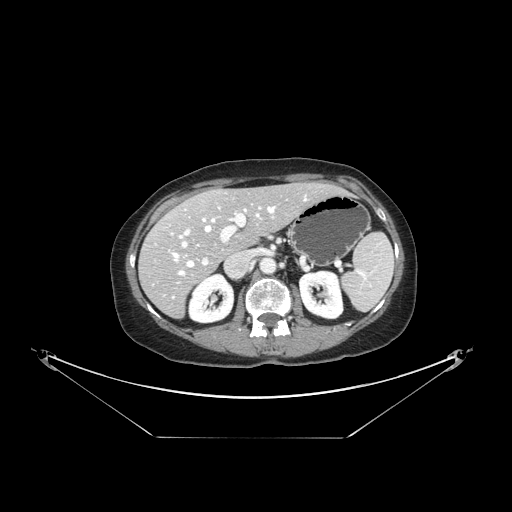
Contrast-enhanced abdominal CT, one axial slice; position 87 of 148 along the scan axis; intravenous contrast given; soft-tissue window (W 400 / L 40 HU); 2.5 mm slice thickness; 512 × 512 image matrix. Female patient, age 73 years. From the clinical record (not read from this slice): diagnosis: colorectal cancer liver metastases, imaged before liver resection; multiple liver metastases: no; largest metastasis: 1 cm; disease in both lobes: no.
Structures marked on this image (expert manual segmentation):
- hepatic veins: bounding box <173,198,306,275> (left, top, right, bottom; pixels)
- liver: <140,184,336,317>
- planned liver remnant (the part of the liver to remain after resection): <168,184,337,253>
- portal vein (with intrahepatic branches): <171,207,261,265>